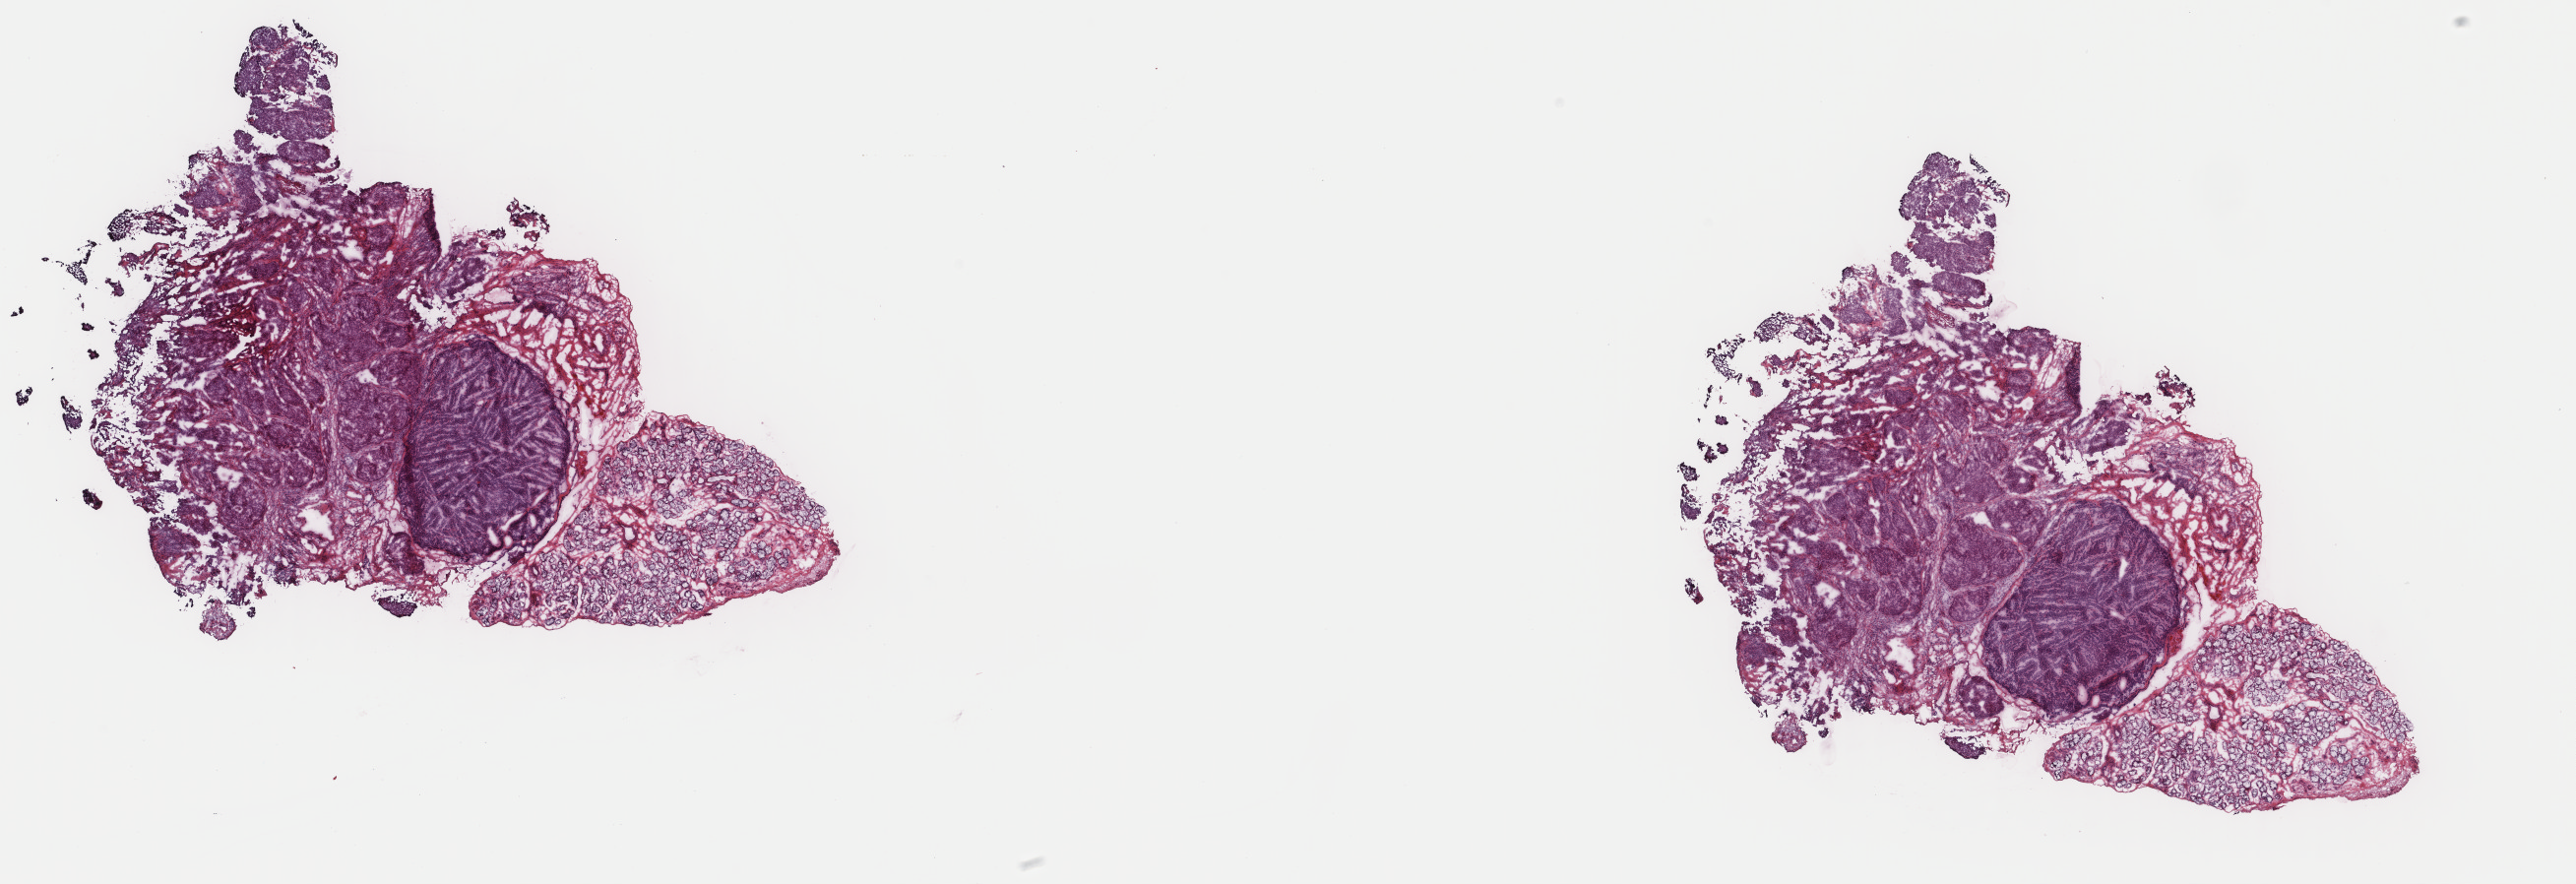
Whole-slide histology image, Hematoxylin and eosin (H&E) stained — whole scanned area (about 20.8 x 7.1 mm) shown as a low-resolution overview, frozen section from the top of the tissue portion, sample: primary tumour, head and neck. Patient: male, age at initial diagnosis 61 years. Histologic grade: GX (grade cannot be assessed). Composition of this section per pathologist review: tumour cells 45%, tumour nuclei 60%, normal cells 55%, stromal cells 0%, necrosis 0%. Inflammatory infiltration, as recorded: lymphocyte infiltration 4%, monocyte infiltration 0%, neutrophil infiltration 0%.
* pathologic diagnosis: Squamous cell carcinoma, large cell, nonkeratinizing, NOS